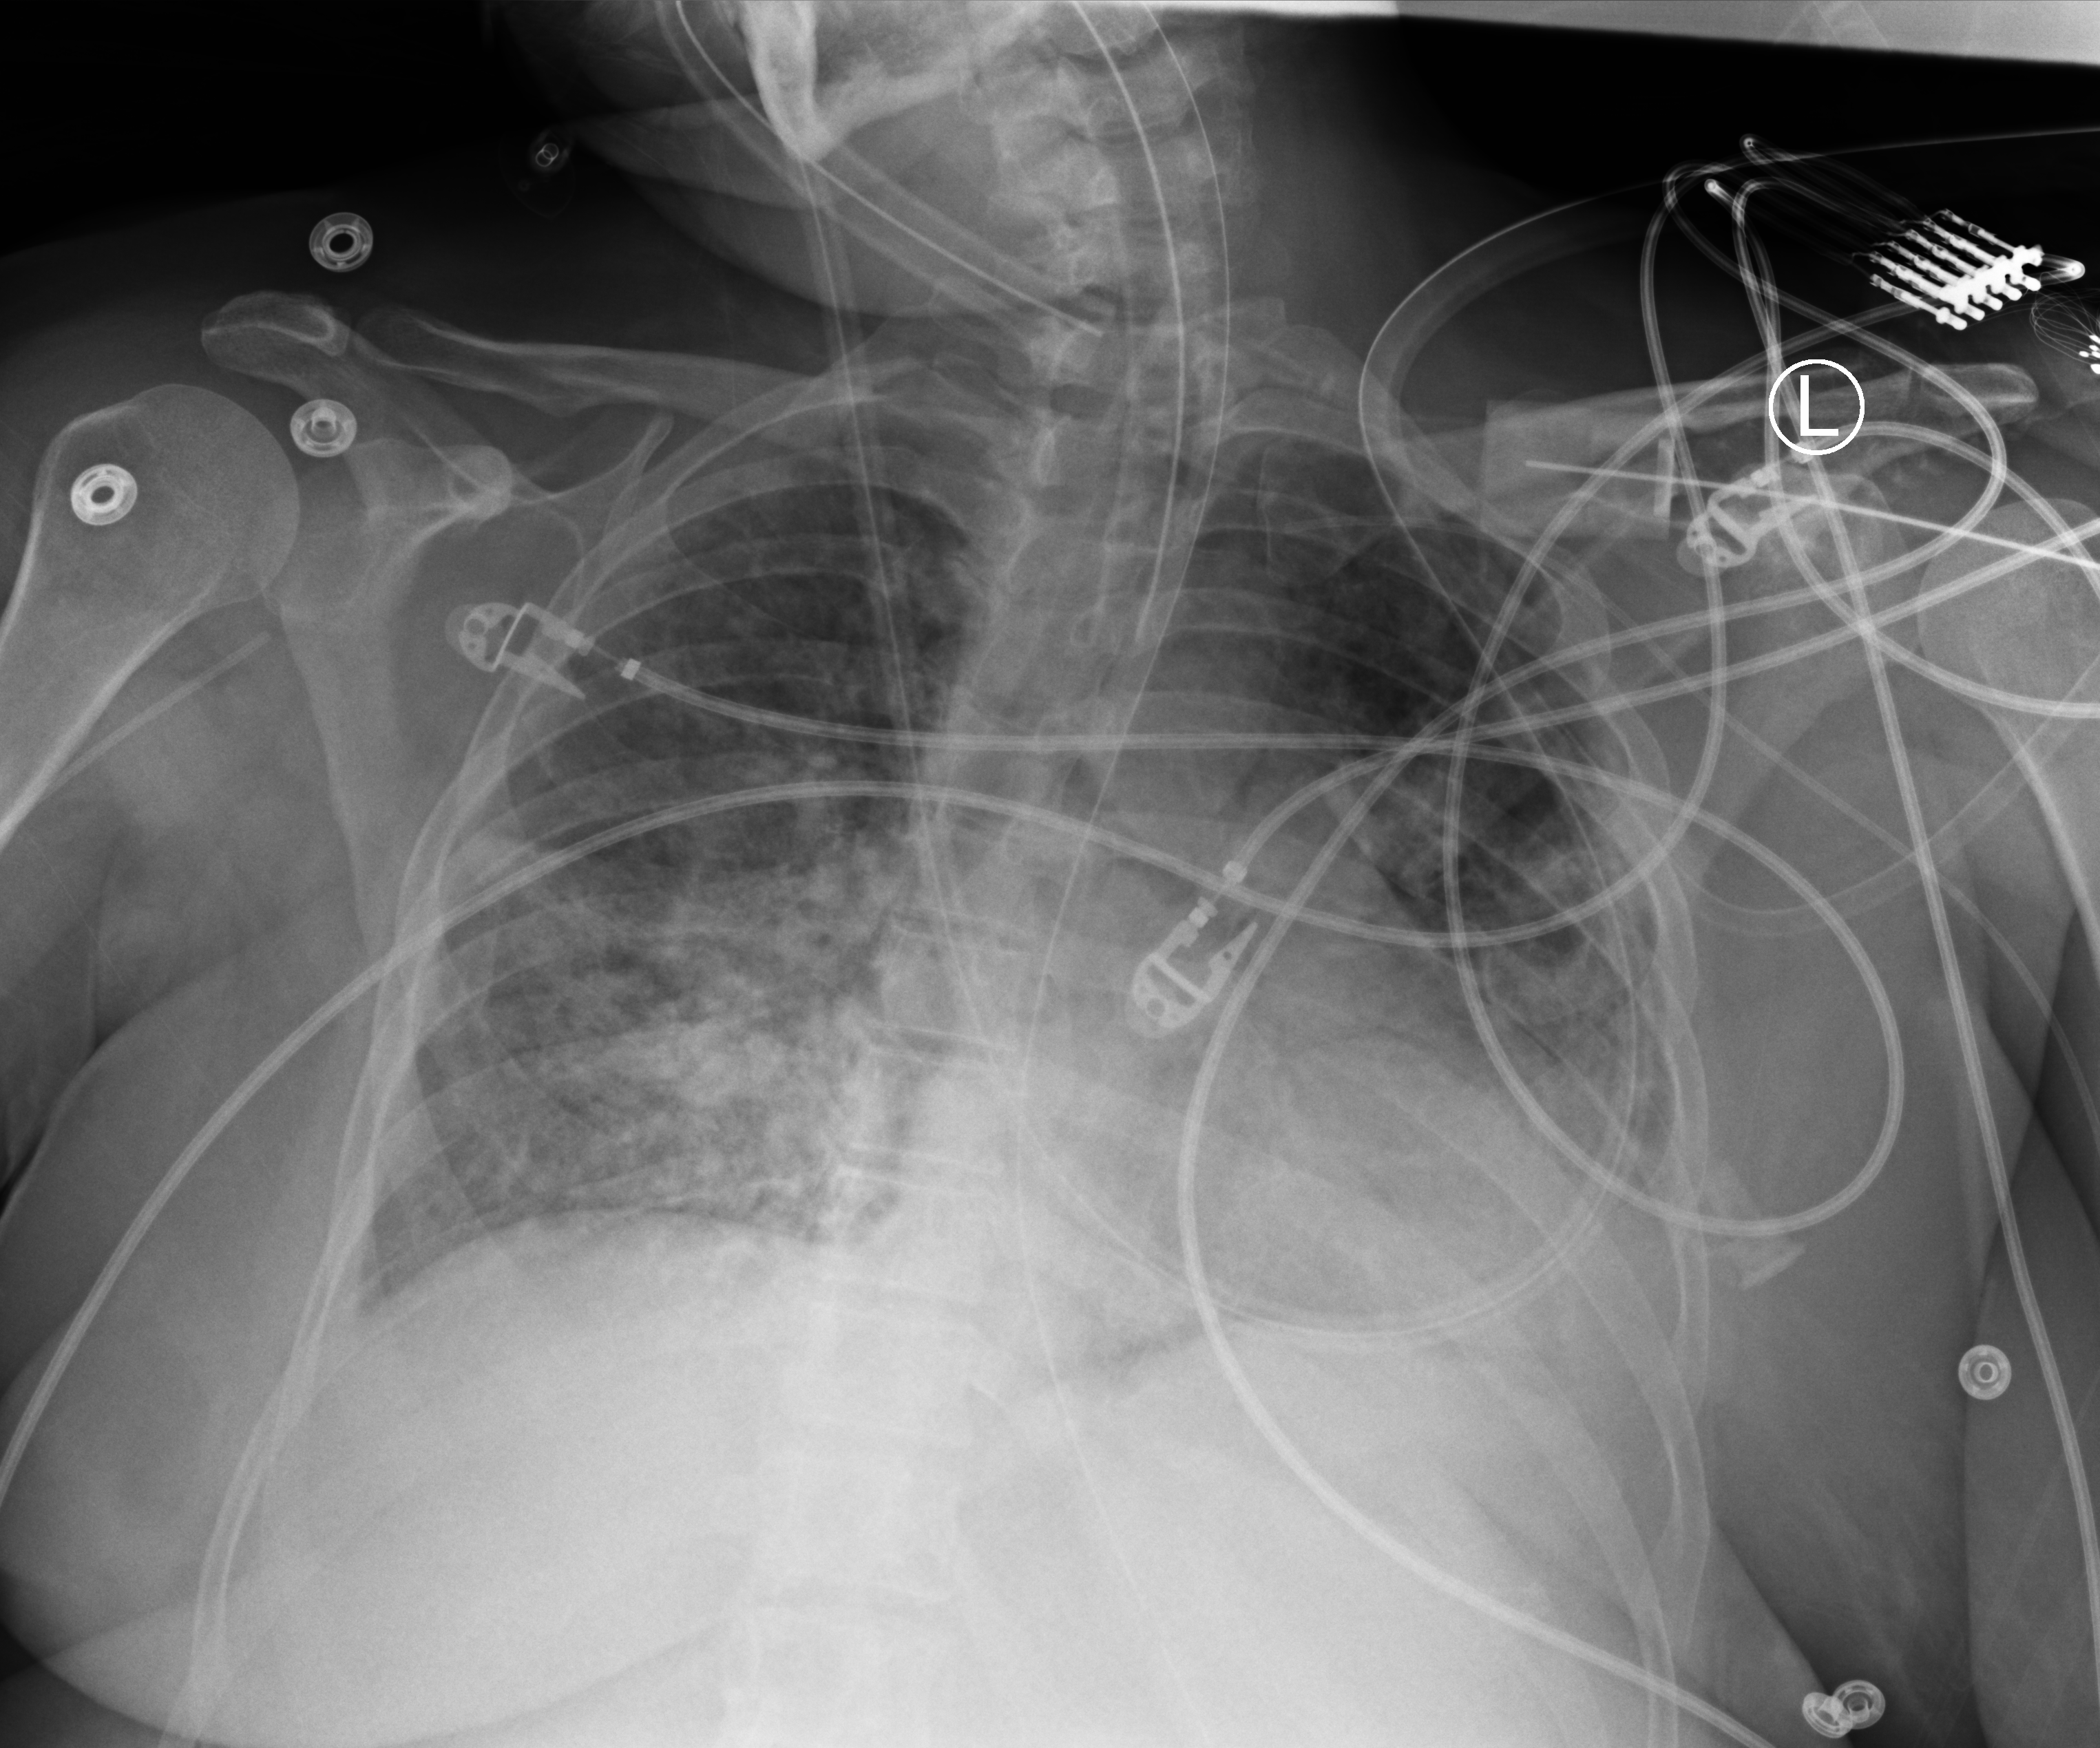
Bedside chest radiograph (computed radiography), anteroposterior (AP) projection. Patient hospitalised with COVID-19; female, aged 18–59 years.
Hospital-stay facts (about this admission, not read from this image; timing relative to this image not recorded):
- mechanically ventilated during this hospital stay: yes
- admitted to intensive care during this hospital stay: yes